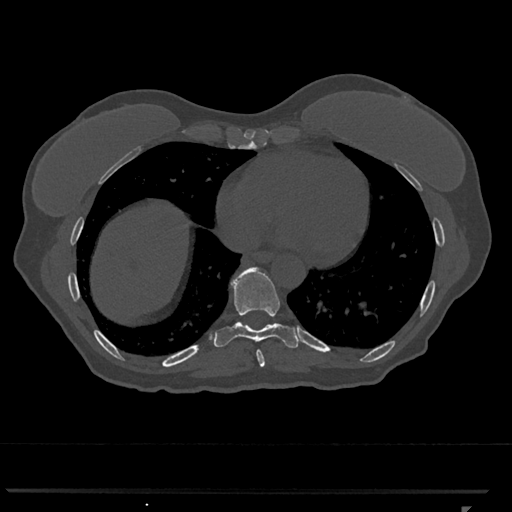
CT including the spine, one axial slice. Reconstruction kernel Br40s/3. 120 kVp. Bone window (W 1800 / L 400 HU). 512 × 512 image matrix, field of view 380 × 380 mm. Female patient, age 62 years. From the clinical record (not read from this slice): primary cancer: renal.
Annotated regions visible in this slice (semi-automatically segmented with operator editing):
- T8 vertebra: bounding box (x1, y1, x2, y2) in pixels: (256, 350, 265, 367)
- T9 vertebra: (214, 267, 300, 348)